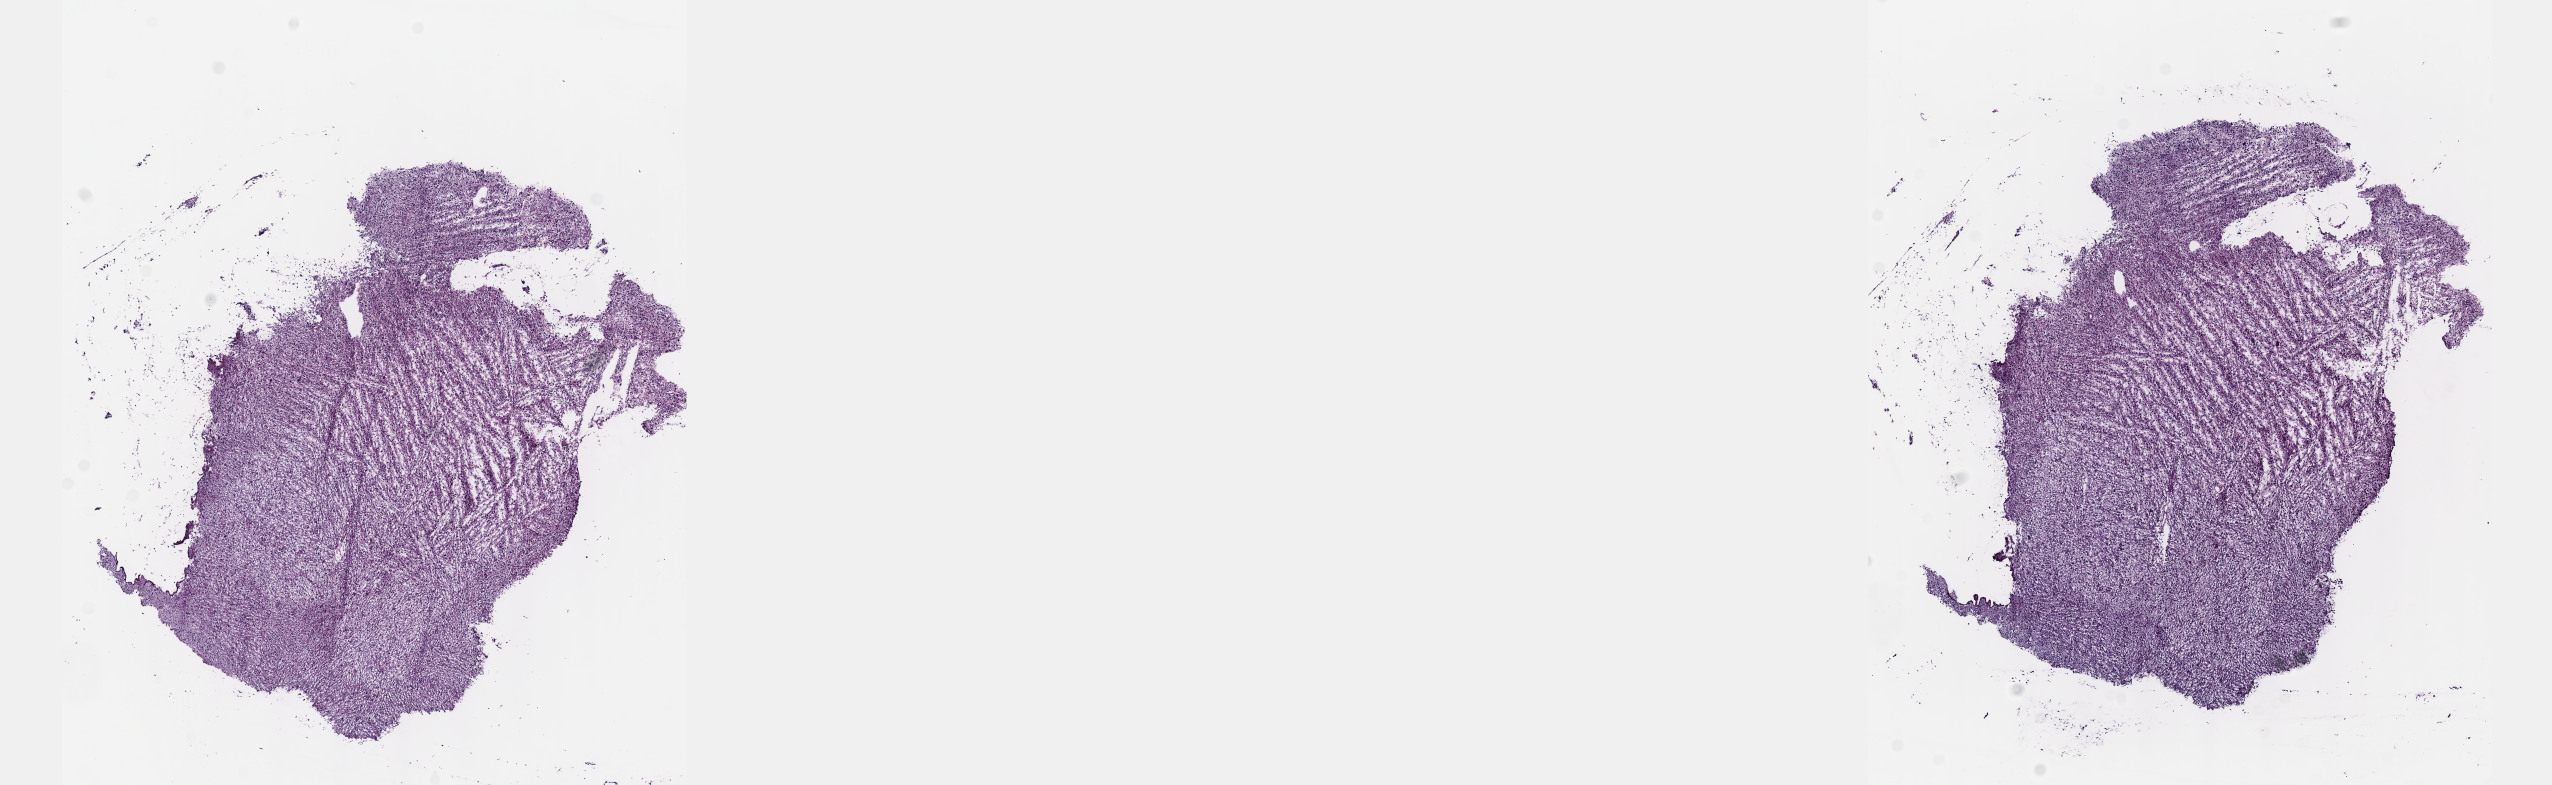
Whole-slide histology image, H&E — a low-resolution overview of the entire scanned area, about 20.6 x 6.3 mm. Frozen section from the top of the tissue portion. Sample: primary tumour, brain. Female patient; age at initial diagnosis 33 years. Histologic grade: G3 (poorly differentiated). Slide review estimates, as recorded: tumour cells 70%, tumour nuclei 90%, normal cells 5%, stromal cells 25%, necrosis 0%. Infiltration values recorded for this section: lymphocyte infiltration 0%, monocyte infiltration 0%, neutrophil infiltration 0%.
Pathologic diagnosis: Astrocytoma, anaplastic (cerebrum). Laterality: right.